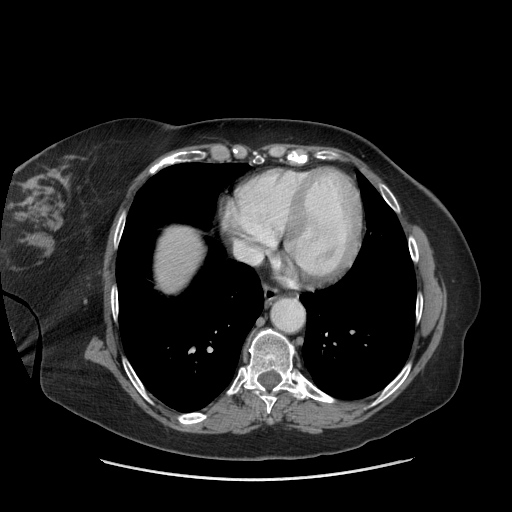
Contrast-enhanced abdominal CT (liver protocol), one axial slice. Slice 69 of 69 in the series (ordered by position). Reconstruction kernel STANDARD. Soft-tissue window (W 400 / L 40 HU). 2.5 mm slice thickness. 512 × 512 image matrix. Case-level facts recorded for this patient, not image findings: diagnosis: hepatocellular carcinoma (patient treated with transarterial chemoembolisation; whether this scan precedes or follows treatment is not stated here); TNM stage (as recorded): Stage-IIIB; Child-Pugh class: A; tumour nodularity: multinodular.
Structures marked on this image (semi-automatic segmentation, software-assisted and operator-edited):
- abdominal aorta: box from (x=272, y=299) to (x=303, y=331) px
- liver parenchyma outside the tumour (the mass and vessels are separate outlines, so this box may not span the whole liver): (x=156, y=226)–(x=200, y=290)